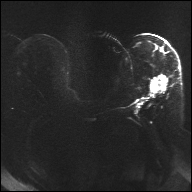
Breast MRI, one axial slice; slice 15 of 32 in the series (ordered by position); diffusion-weighted series; image 2 of 4 stored at this slice position (different b-values; order by instance number); 1.5 T; 4 mm slice thickness; 192 × 192 image matrix, field of view 360 × 360 mm. Female patient.
Structures marked on this image (manually delineated by an expert):
- tumour on diffusion-weighted imaging: bounding box <152,75,167,92> (left, top, right, bottom; pixels)